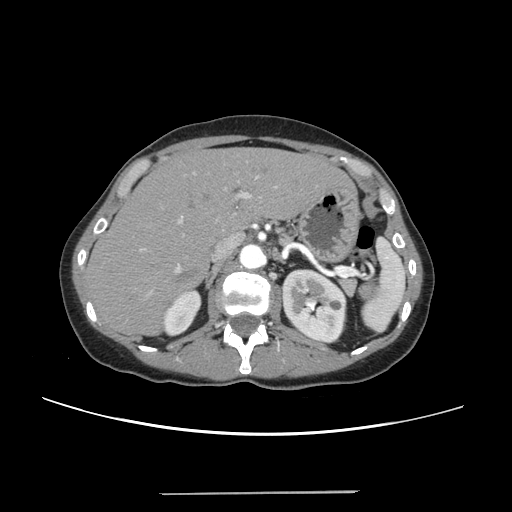
Contrast-enhanced abdominal CT, one axial slice; position 162 of 240 along the scan axis; 120 kVp; soft-tissue window (W 400 / L 40 HU); 1.25 mm slice thickness; 512 × 512 image matrix, field of view 371 × 371 mm. Female patient, age 60 years. Case-level facts recorded for this patient, not image findings: diagnosis: colorectal cancer liver metastases, imaged before liver resection; multiple liver metastases: no; largest metastasis: 1.5 cm; disease in both lobes: no.
Annotated regions visible in this slice (expert manual segmentation):
- liver: box from (x=88, y=147) to (x=348, y=334) px
- planned liver remnant (the part of the liver to remain after resection): (x=87, y=148)–(x=347, y=334)
- portal vein (with intrahepatic branches): (x=139, y=171)–(x=259, y=295)